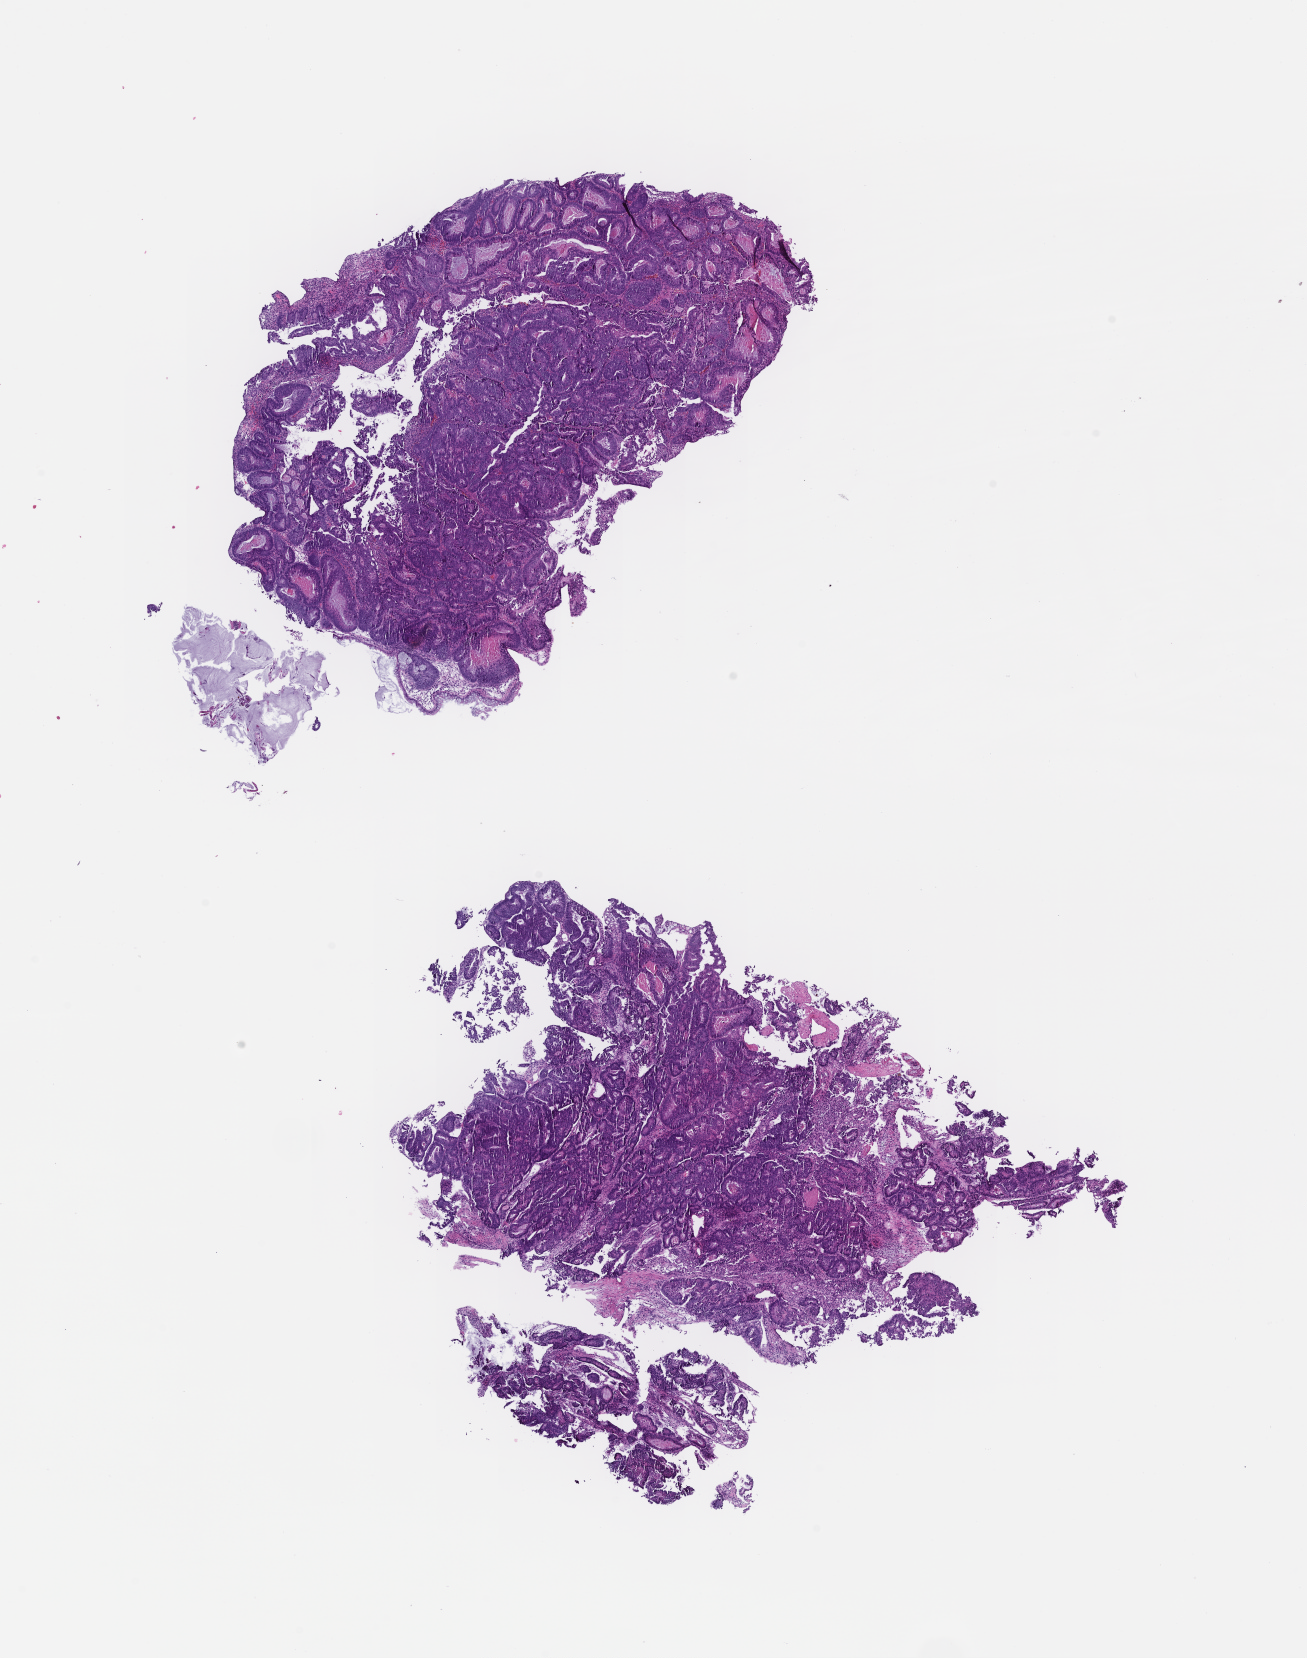
Whole-slide image, H&E stain, low-resolution overview of the scanned area, about 10.6 x 13.4 mm, formalin-fixed, paraffin-embedded (FFPE) tissue, tissue site: colon, archival tissue. Patient sex: male.
This section: primary tumour tissue. Diagnosis: Colorectal Carcinoma.